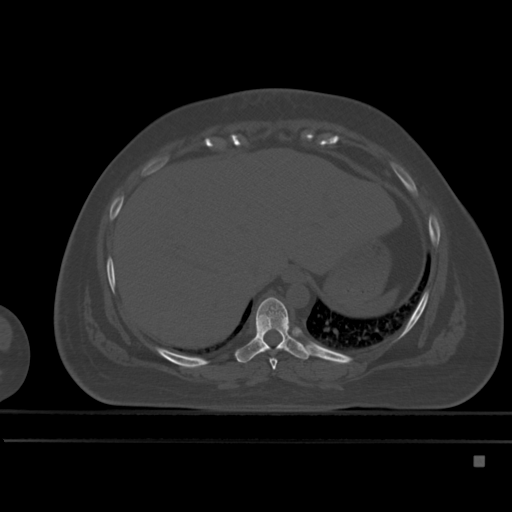
CT including the spine, one axial slice. Slice 265 of 495 in the series (ordered by position). Bone window (W 1800 / L 400 HU). 512 × 512 image matrix. Female patient, age 33 years. From the clinical record (not read from this slice): primary cancer: breast; vertebrae with lytic lesions (as recorded): T1.
Outlined on this slice (semi-automatic segmentation, software-assisted and operator-edited):
- T8 vertebra: box from (x=270, y=358) to (x=277, y=370) px
- T9 vertebra: (x=235, y=297)–(x=310, y=363)